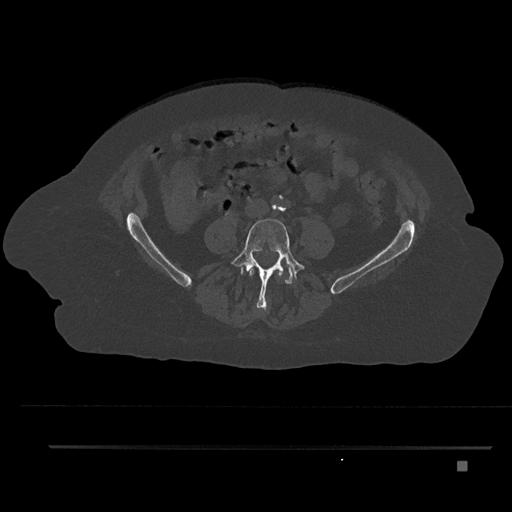
CT including the spine, one axial slice. Position 81 of 797 along the scan axis. Reconstruction kernel Br40s/3. 120 kVp. Bone window (W 1800 / L 400 HU). 0.5 mm slice thickness. 512 × 512 image matrix. Patient: female, 76 years. Case-level facts recorded for this patient, not image findings: primary cancer: lung; vertebrae with lytic lesions (as recorded): T11, L3.
Structures marked on this image (semi-automatically segmented with operator editing):
- L3 vertebra: bounding box [x1, y1, x2, y2] px = [249, 268, 283, 278]
- L4 vertebra: [231, 218, 306, 311]
- L5 vertebra: [242, 264, 296, 284]